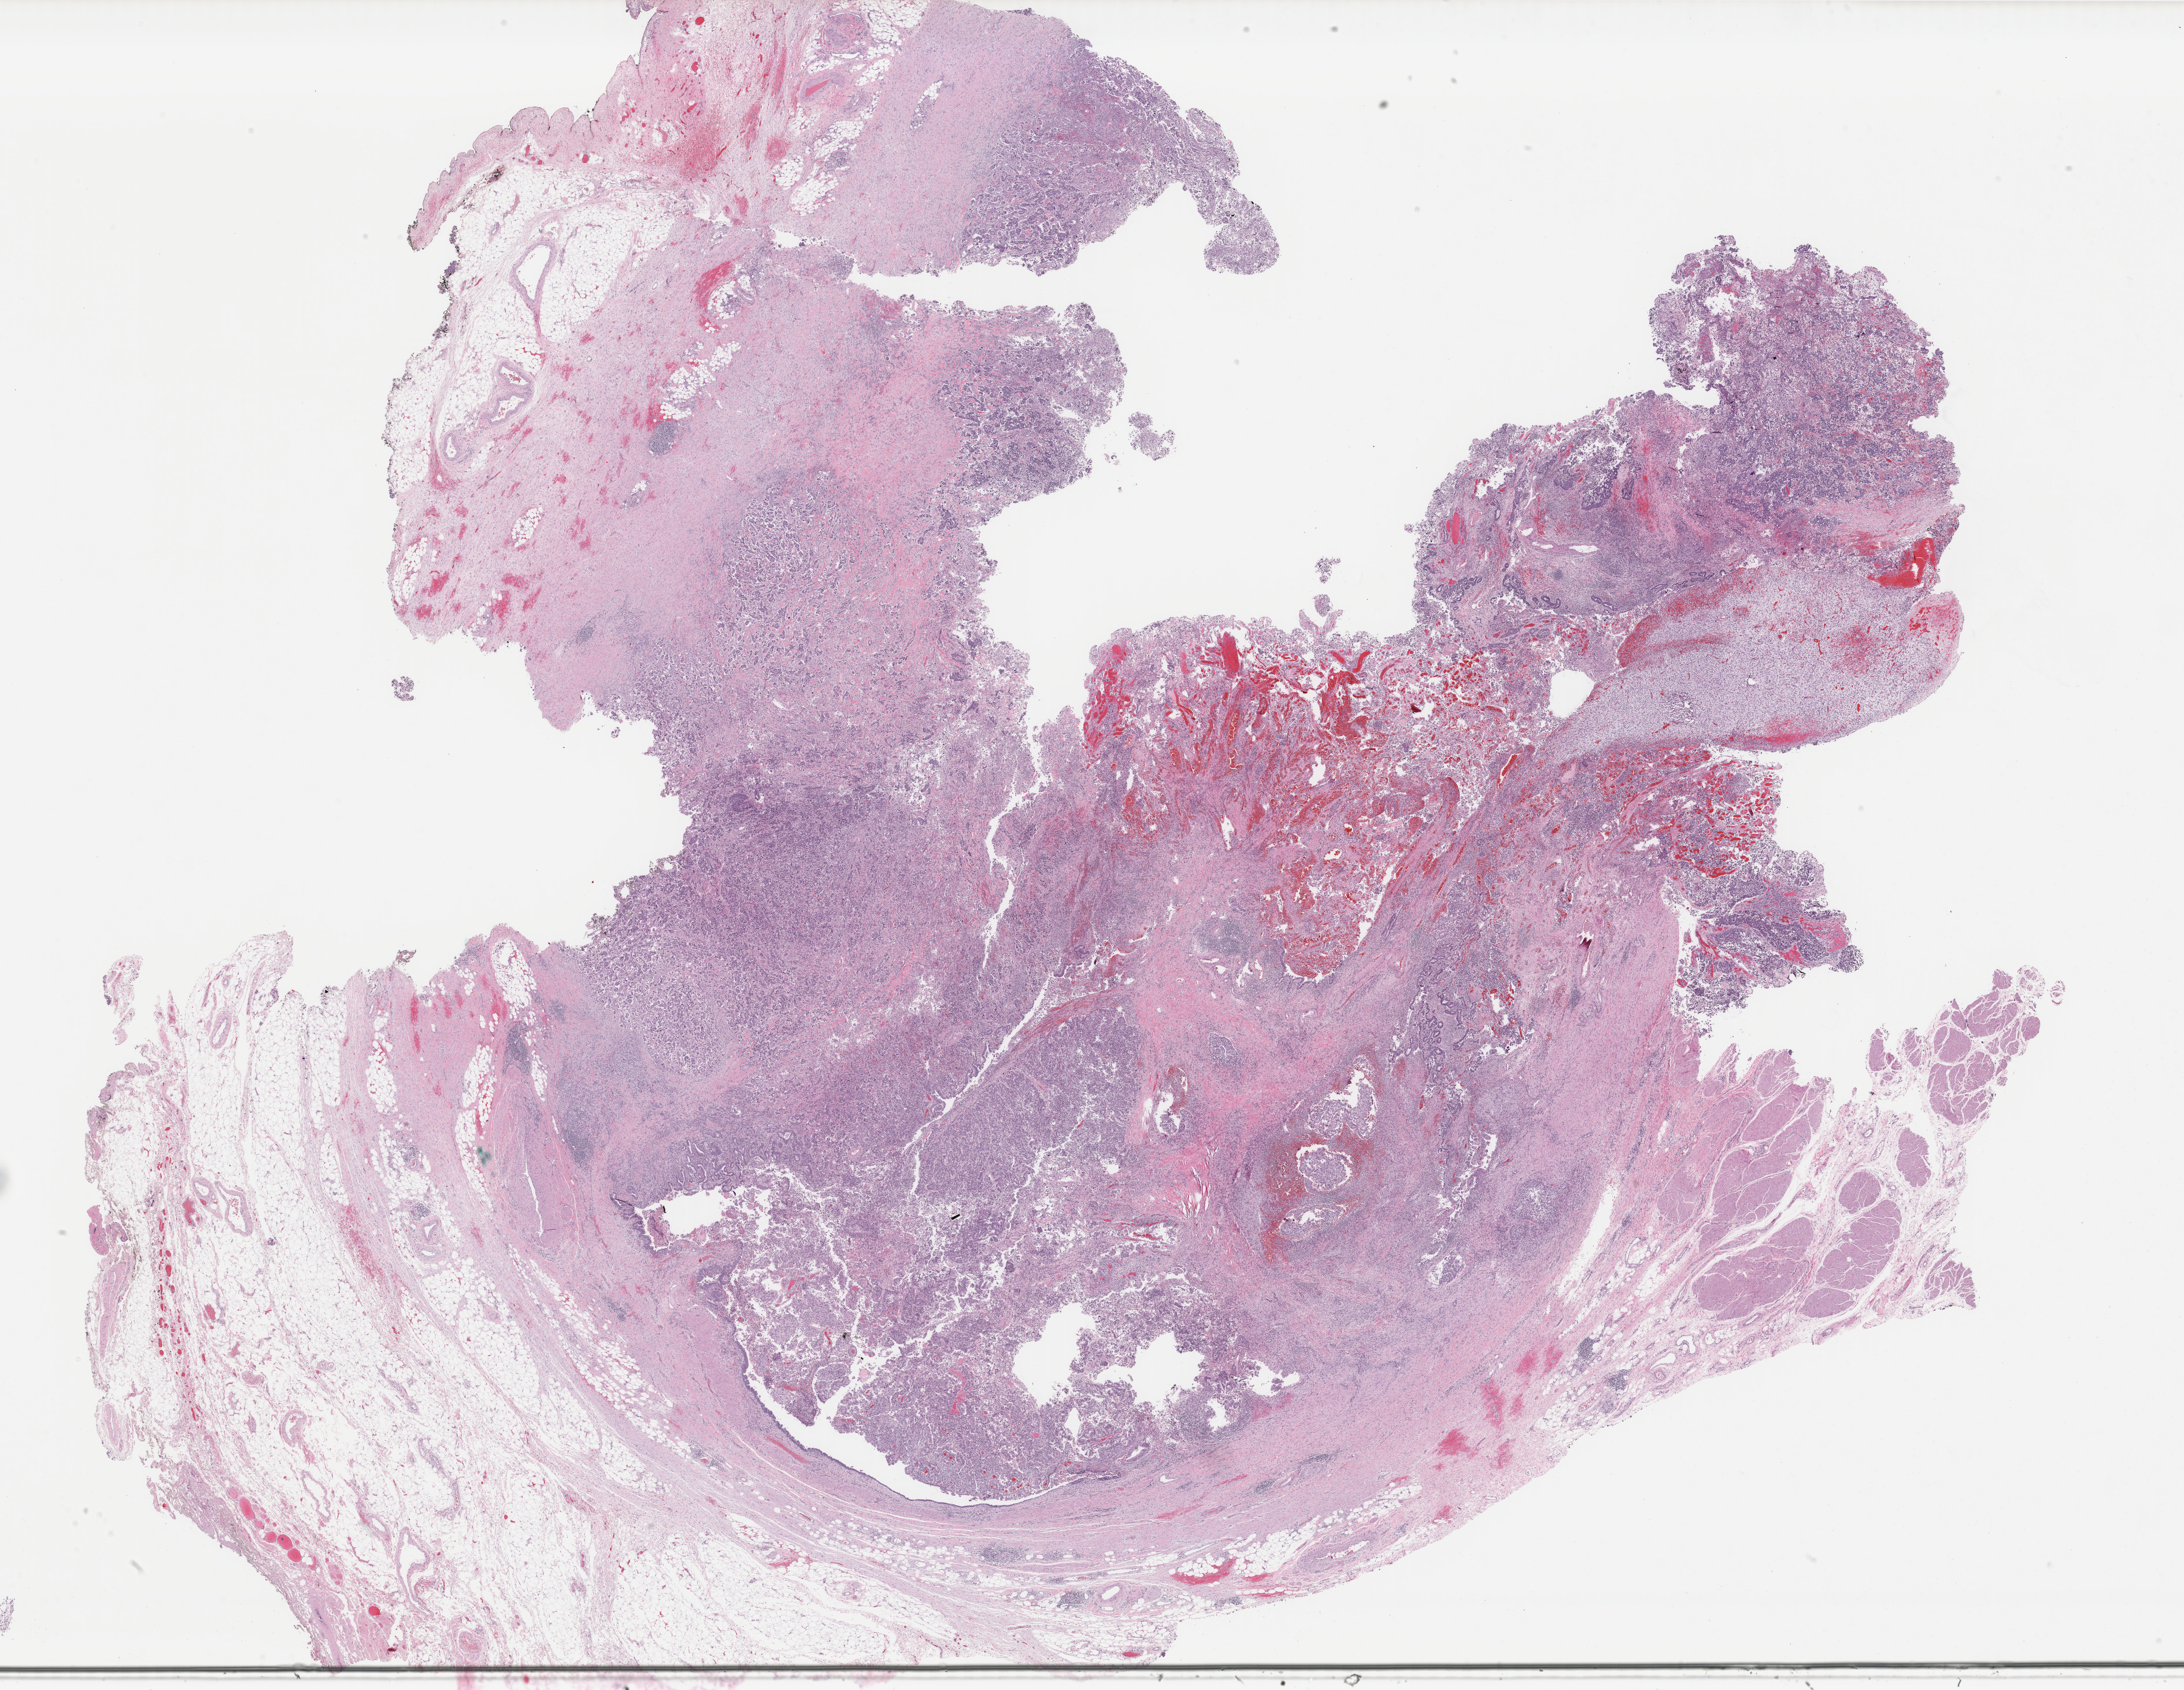
Digitized H&E tissue section (whole slide) — low-resolution overview of the scanned area, about 30.0 x 23.2 mm, formalin-fixed paraffin-embedded (FFPE) diagnostic section, sample: primary tumour, bladder. Patient: male, age at initial diagnosis 72 years. Histologic grade: high grade.
* lymph nodes positive (case pathology): 1 of 14 examined
* AJCC pathologic stage: IV (7th edition)
* histologic diagnosis: Transitional cell carcinoma